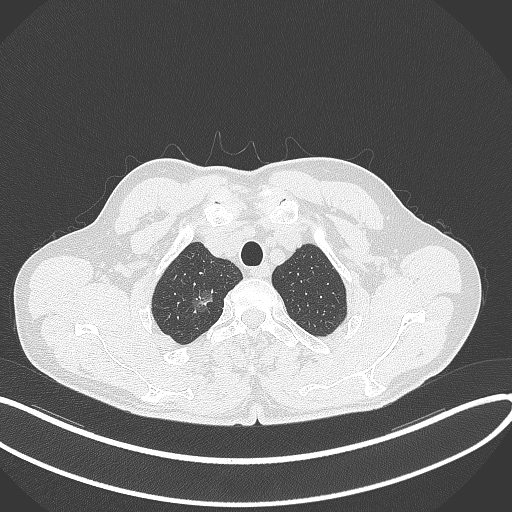
Chest CT, one axial slice; slice 340 of 407 in the series (ordered by position); reconstruction kernel B70f; 120 kVp; lung window (W 1500 / L -600 HU); 512 × 512 image matrix, field of view 400 × 400 mm. Male patient, age 58 years. From the clinical record (not read from this slice): clinical TNM (as recorded): T1c N0 M0.
Outlined on this slice (rectangle marked by the reading radiologist):
- lung tumour (recorded histology: adenocarcinoma): bounding box (x1, y1, x2, y2) in pixels: (193, 283, 218, 311)